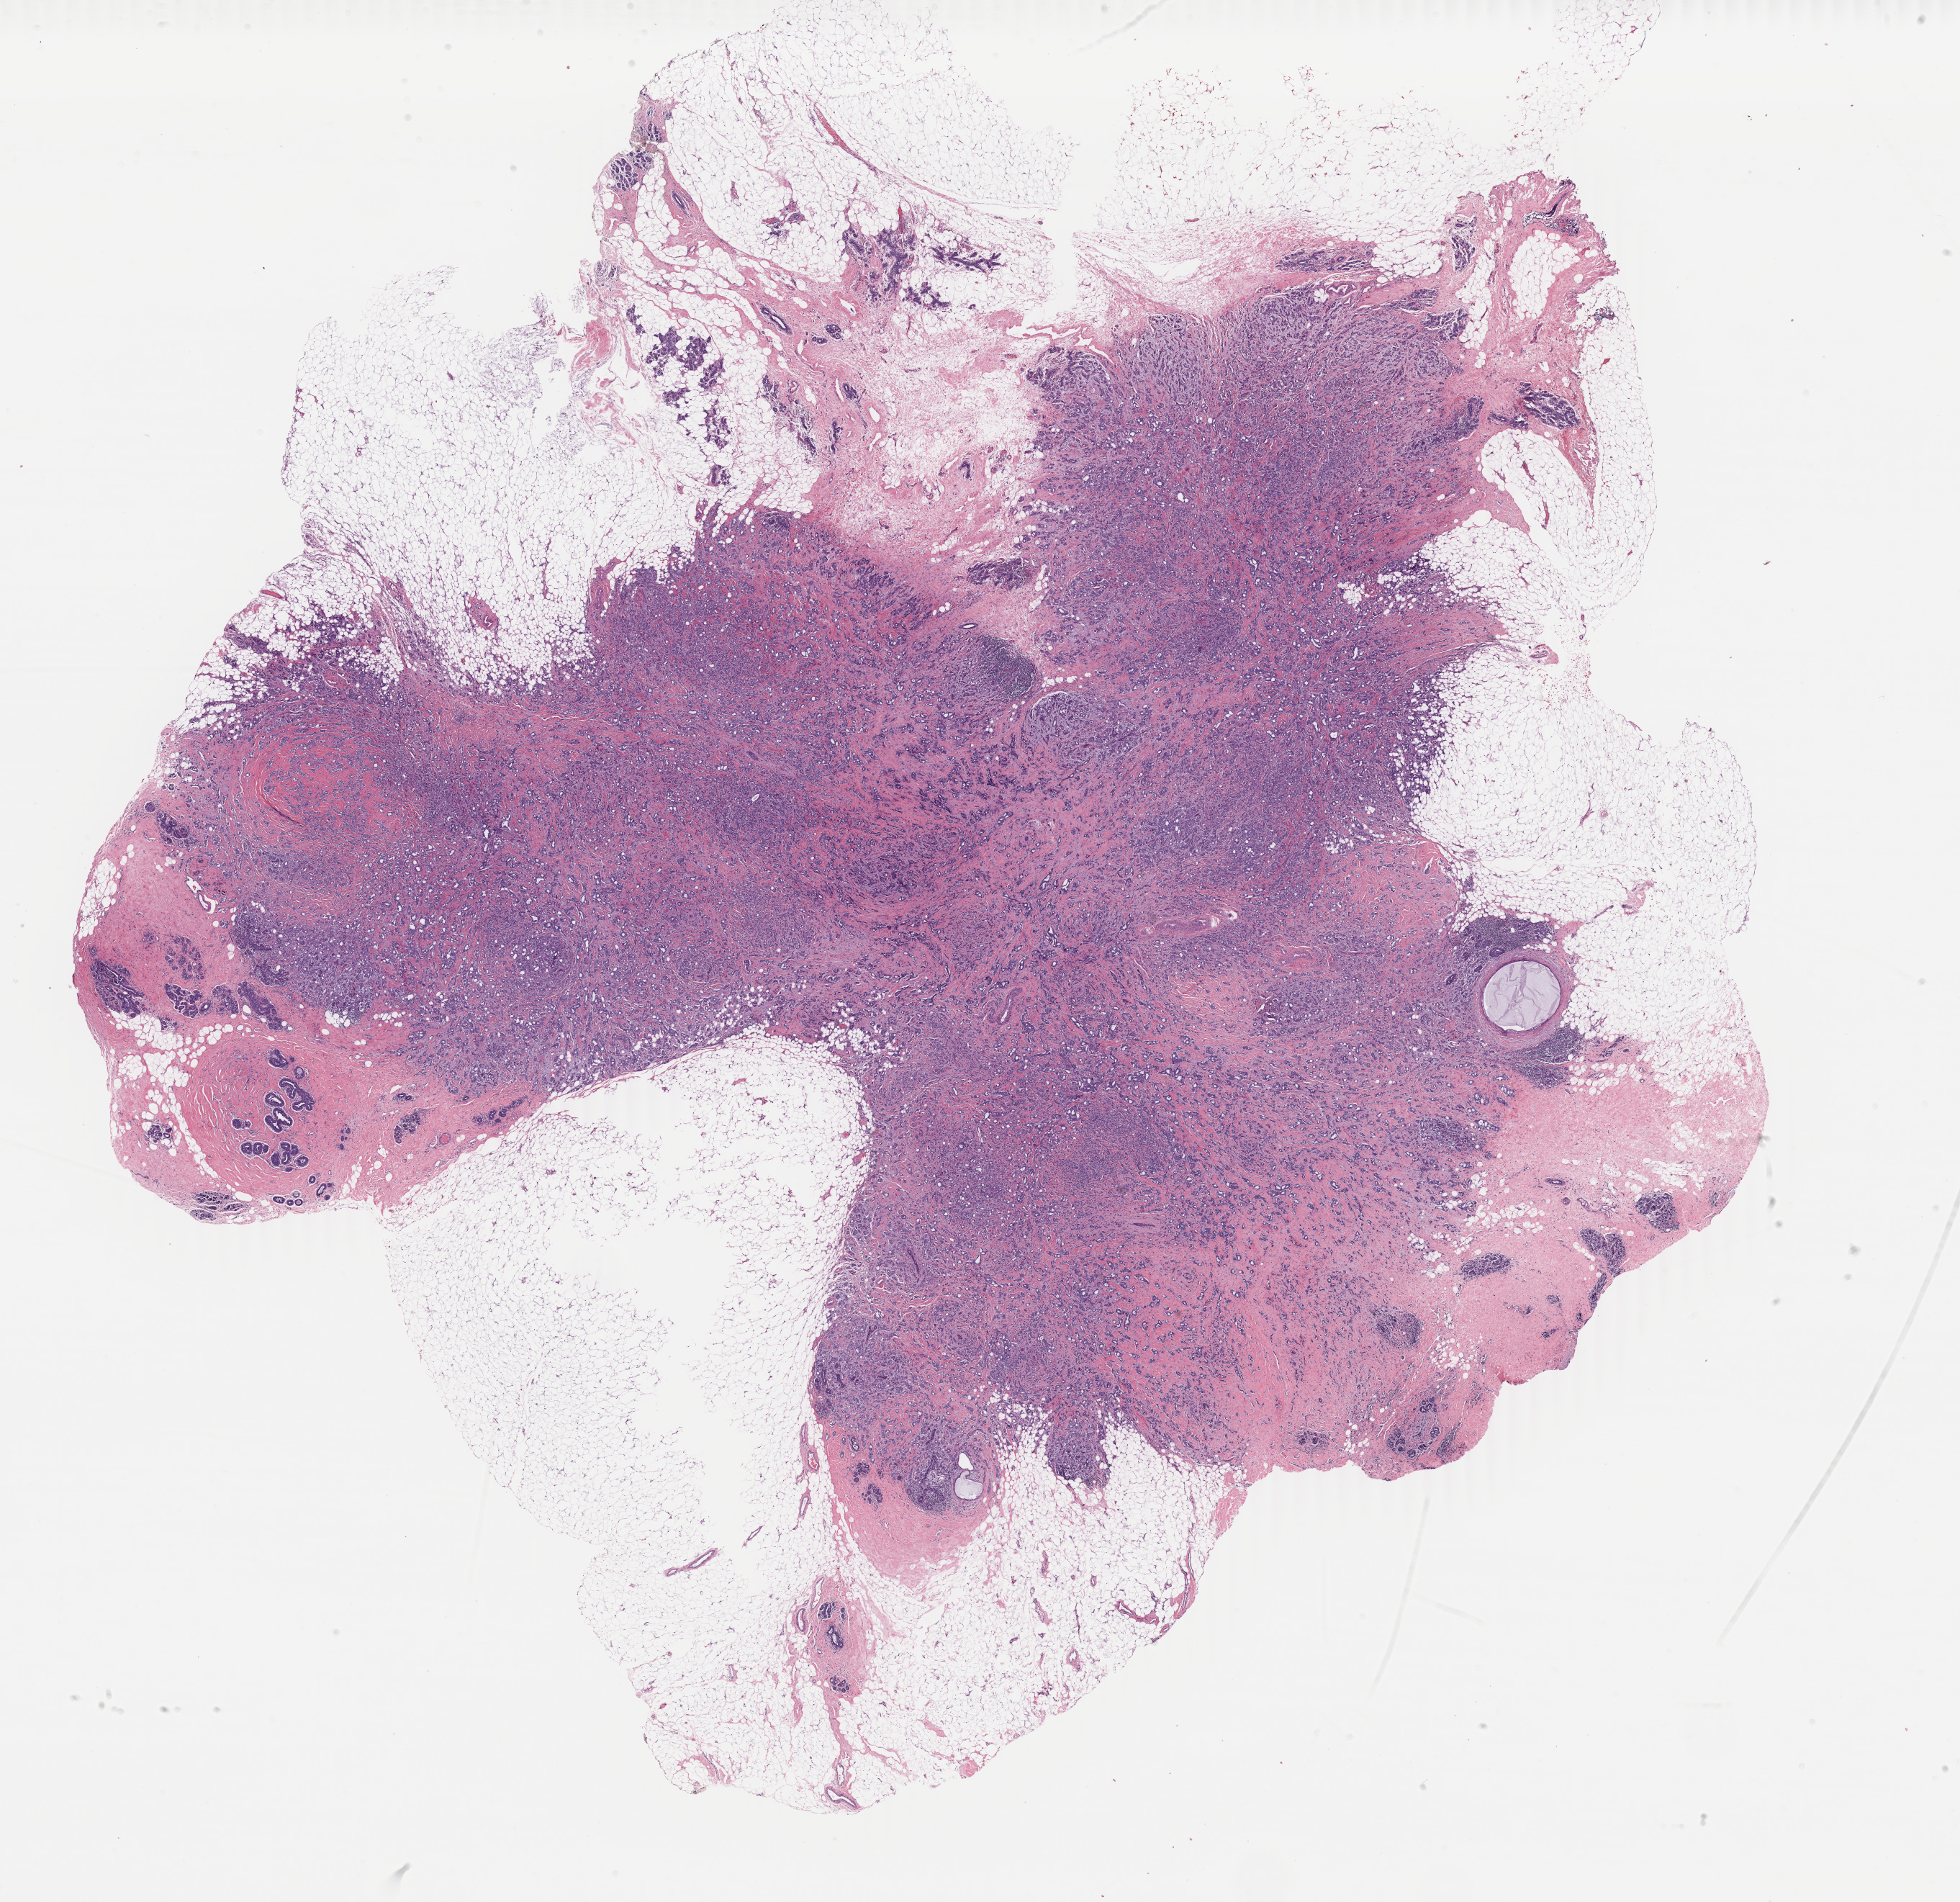
Digitized H&E-stained tissue section (whole slide) — a low-resolution overview of the entire scanned area, about 21.7 x 21.0 mm, formalin-fixed paraffin-embedded (FFPE) diagnostic section, breast, primary tumour sample. Female patient; age at initial diagnosis 49 years.
• laterality: left
• histologic diagnosis: Infiltrating duct carcinoma, NOS
• AJCC pathologic stage: IIB (7th edition)